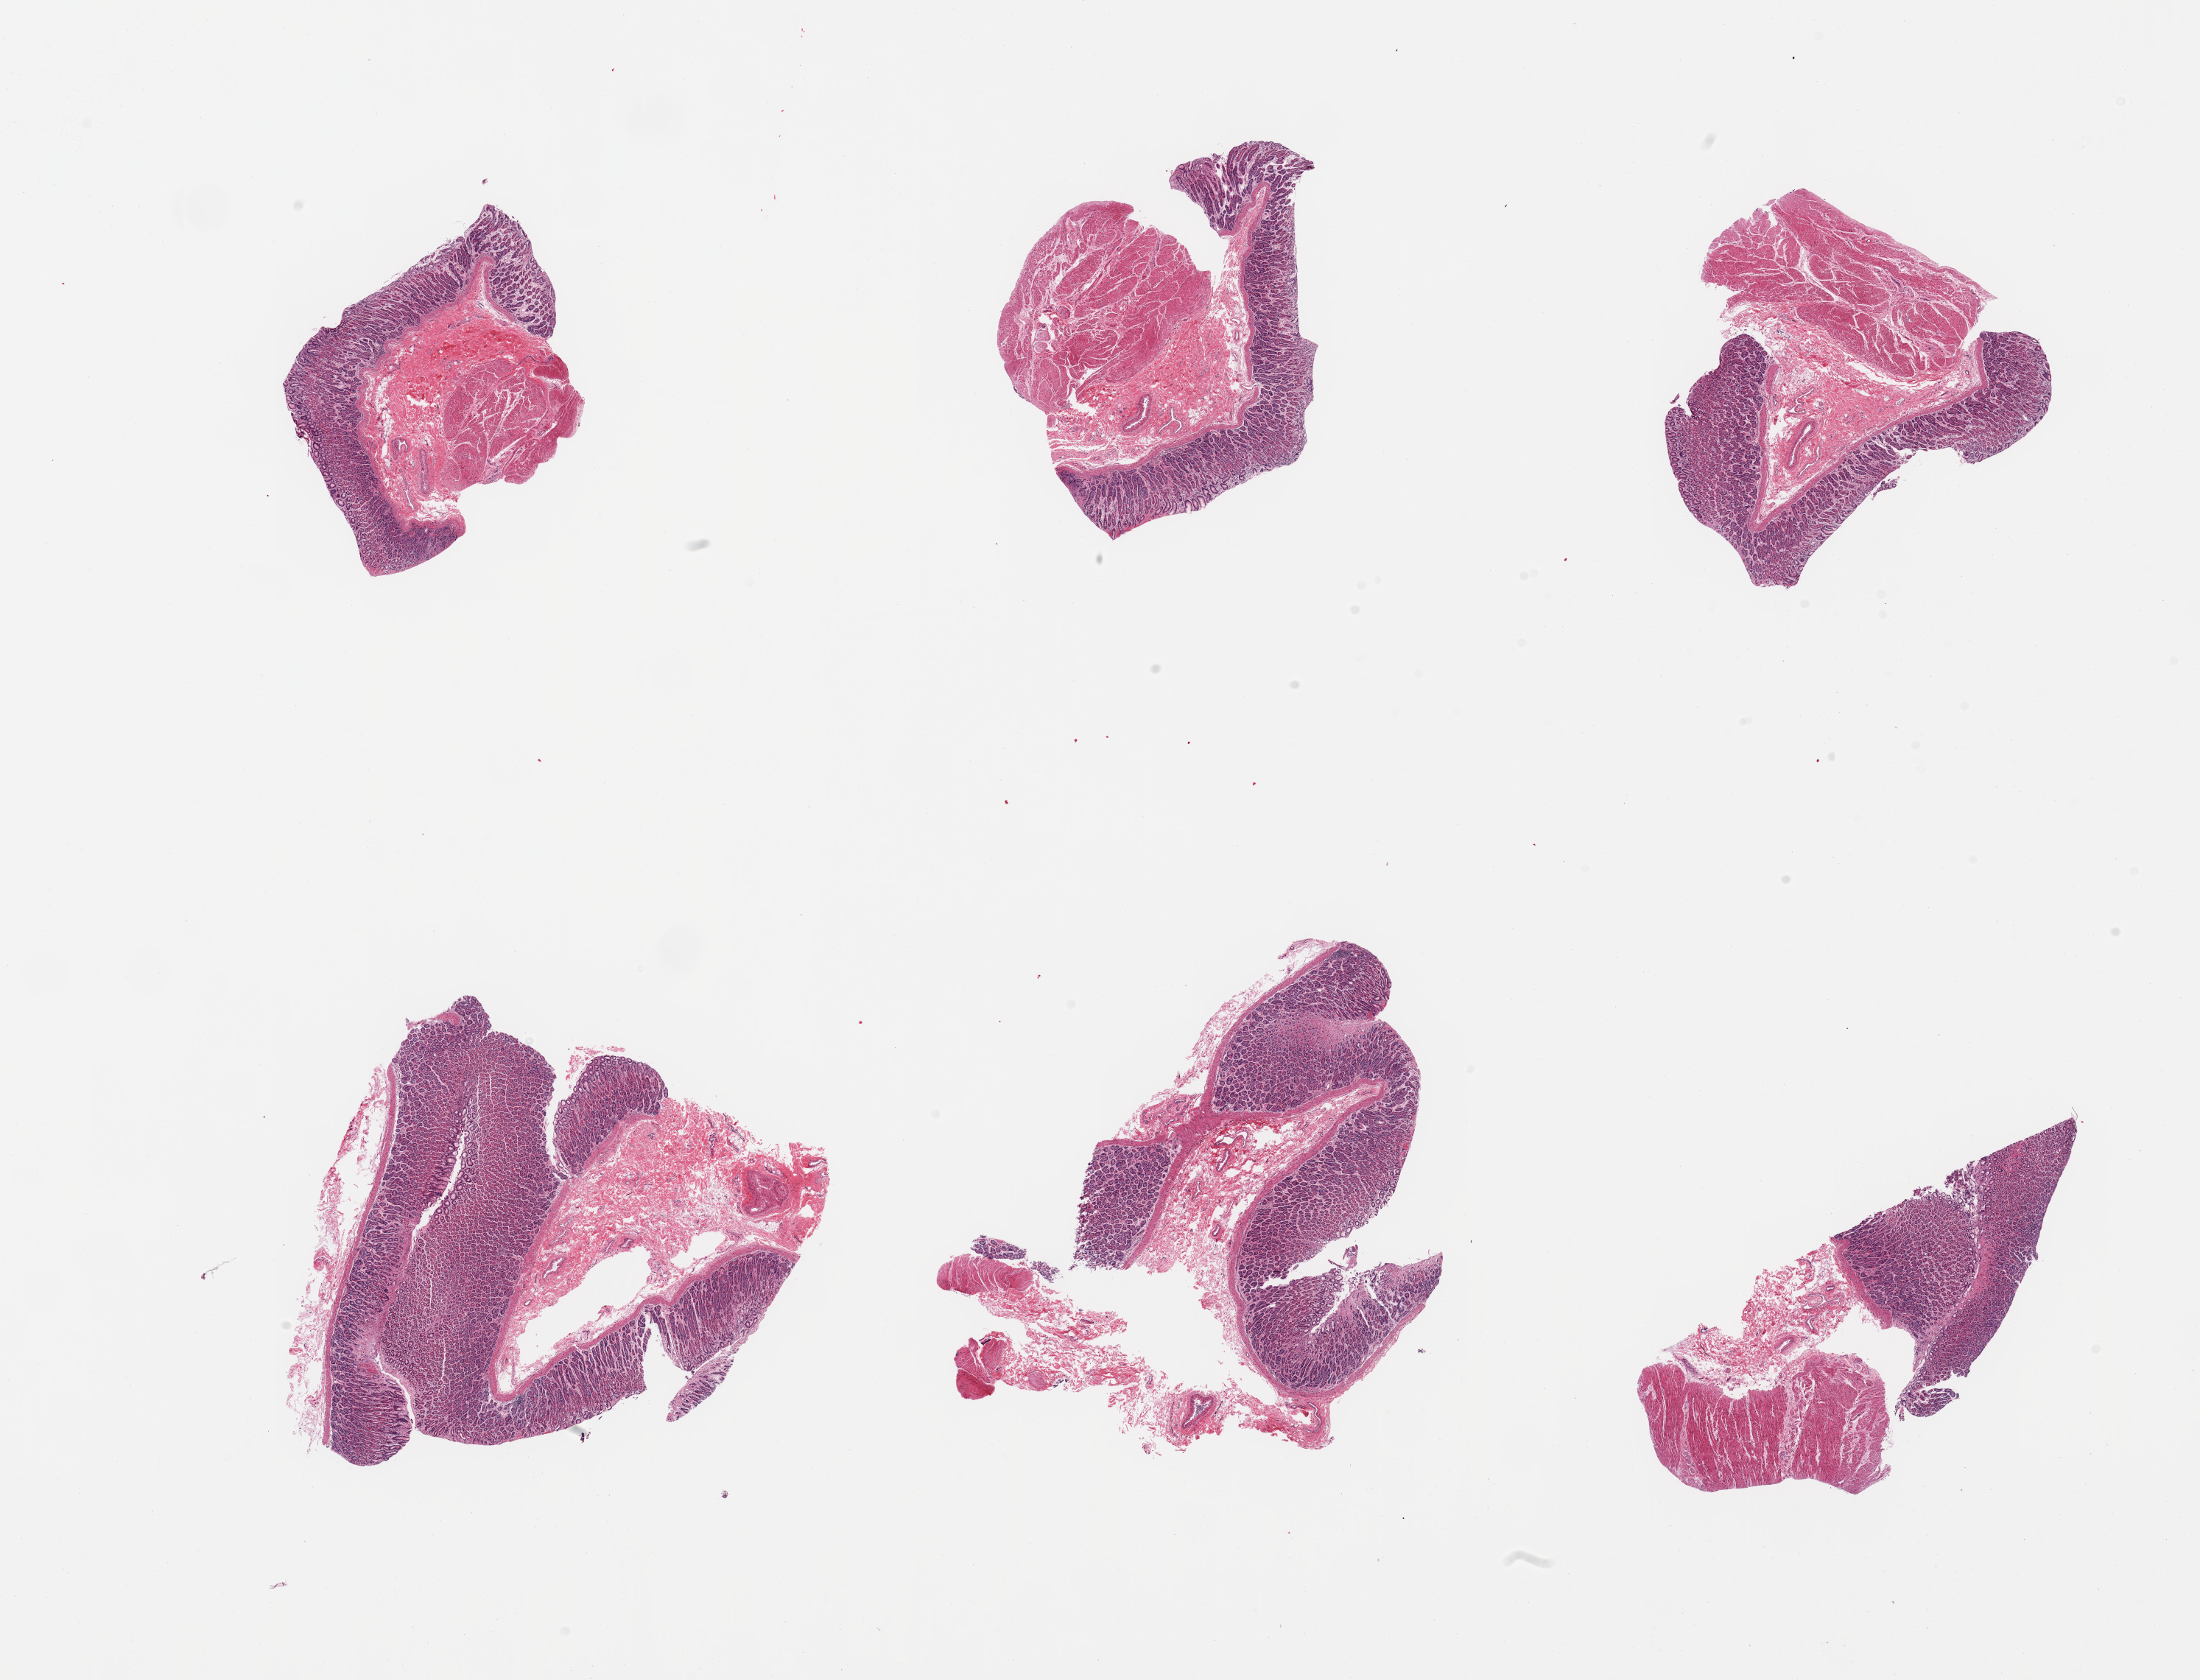
Whole-slide image, hematoxylin and eosin (H&E) stain — low-resolution overview of the scanned area, about 23.6 x 18.0 mm (slide scanned at 20x), PAXgene-fixed paraffin-embedded (PFPE) section, target tissue: stomach, tissue donor sample. Donor sex: female.
Reviewer comment on this tissue sample: 6 pieces; variable representation of mucosa, submucosa, muscularis; focal superficial hemorrhage.